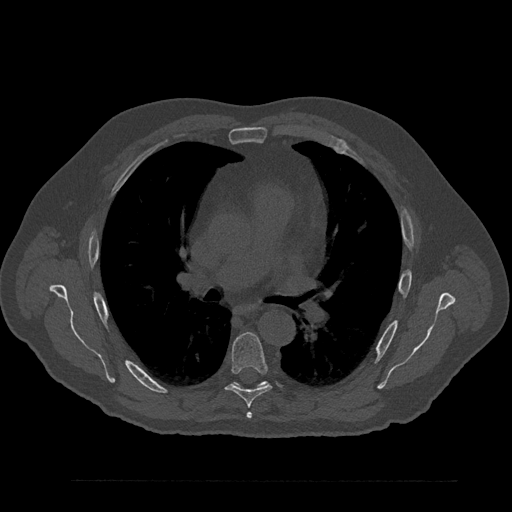
CT including the spine, one axial slice; slice 550 of 797 in the series (ordered by position); 120 kVp; bone window (W 1800 / L 400 HU); 0.5 mm slice thickness; 512 × 512 image matrix, field of view 430 × 430 mm. Male patient, age 61 years. Case-level facts recorded for this patient, not image findings: primary cancer: prostate.
Structures marked on this image (semi-automatic segmentation, software-assisted and operator-edited):
- T5 vertebra: bounding box [x1, y1, x2, y2] px = [247, 413, 252, 418]
- T6 vertebra: [226, 332, 272, 408]
- T7 vertebra: [235, 381, 267, 386]